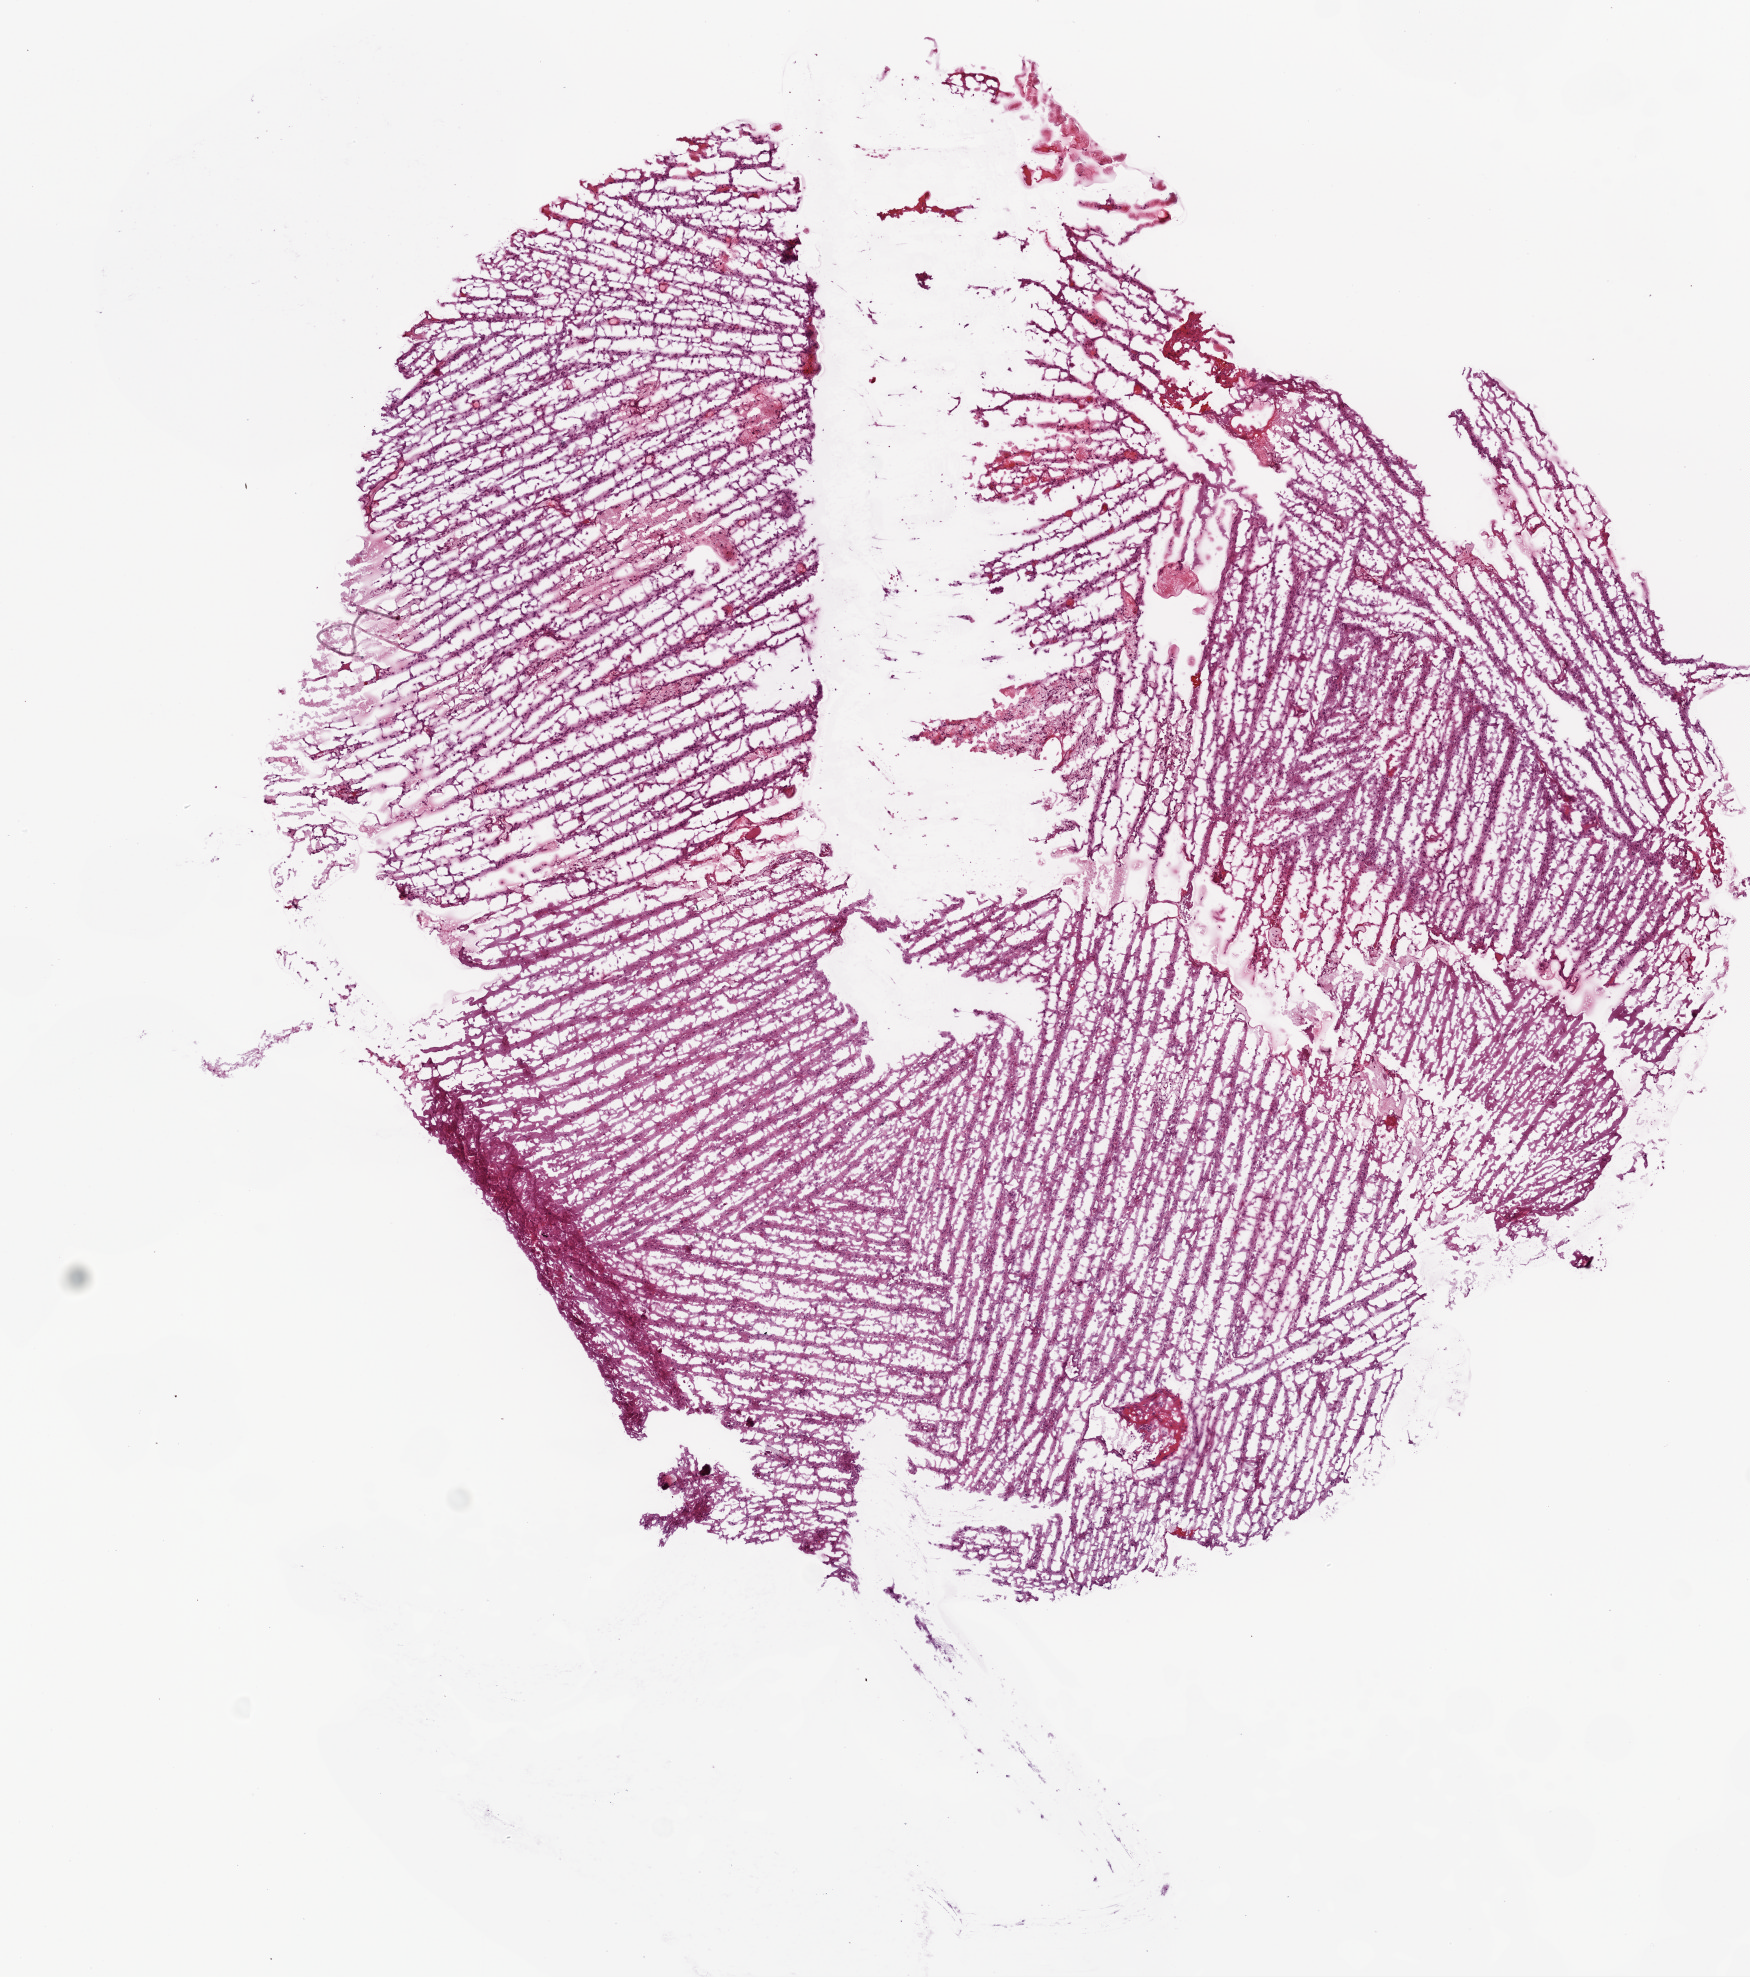
H&E-stained whole-slide image — shown as a low-resolution overview of the whole scanned area (about 7.0 x 7.9 mm, slide scanned at 20x). Frozen section from the top of the tissue portion. Brain, primary tumour sample. Male patient; age at initial diagnosis 61 years. Slide review estimates, as recorded: tumour cells 90%, tumour nuclei 85%, normal cells 5%, stromal cells 5%, necrosis 0%.
- histologic diagnosis: Glioblastoma